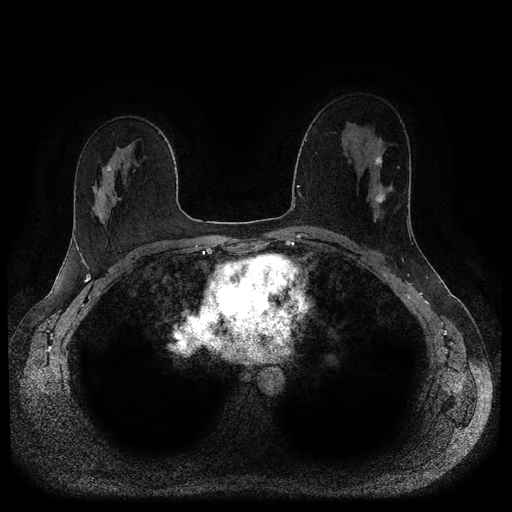
Breast MRI (dynamic contrast-enhanced, multi-phase), one axial slice; position 61 of 116 along the scan axis; dynamic contrast-enhanced series, time point 2 of 5 at this slice position (early post-contrast); 1.5 T; TE 2.6 ms, TR 5.3 ms; 2 mm slice thickness; 512 × 512 image matrix. Female patient, age 45 years.
Structures marked on this image (semi-automatically segmented with operator editing):
- breast lesion (labelled 'tumour' in the annotation; benign lesions carry a separate 'benign' label): bounding box <375,156,386,204> (left, top, right, bottom; pixels)